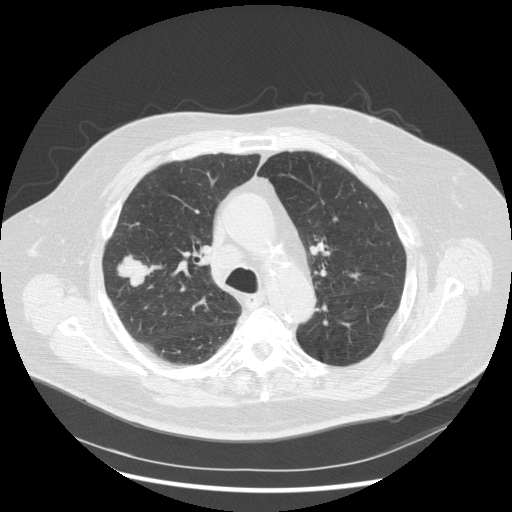
Chest CT (low-dose screening protocol), one axial image, third screening round (two years after baseline), lung window (W 1500 / L -600 HU), standard (soft-tissue) reconstruction kernel (STANDARD), 512 × 512 image matrix. Male, age 72 years at enrolment. Former smoker at enrolment.
Lesion marked by an expert reader, bounding box (x1, y1, x2, y2) in pixels: (101, 250, 157, 298). The exam's reader record, not a measurement of the box and not confirmed to be the same lesion: non-calcified nodule or mass ≥4 mm, right upper lobe, 31 × 31 mm, poorly defined margins, soft tissue attenuation, pre-existing on the prior screen: no. Lung cancer was diagnosed 70 days after this screen: squamous cell carcinoma, NOS, right upper lobe, poorly differentiated (G3), stage IIIA (AJCC 6th edition), 19 mm at pathology.